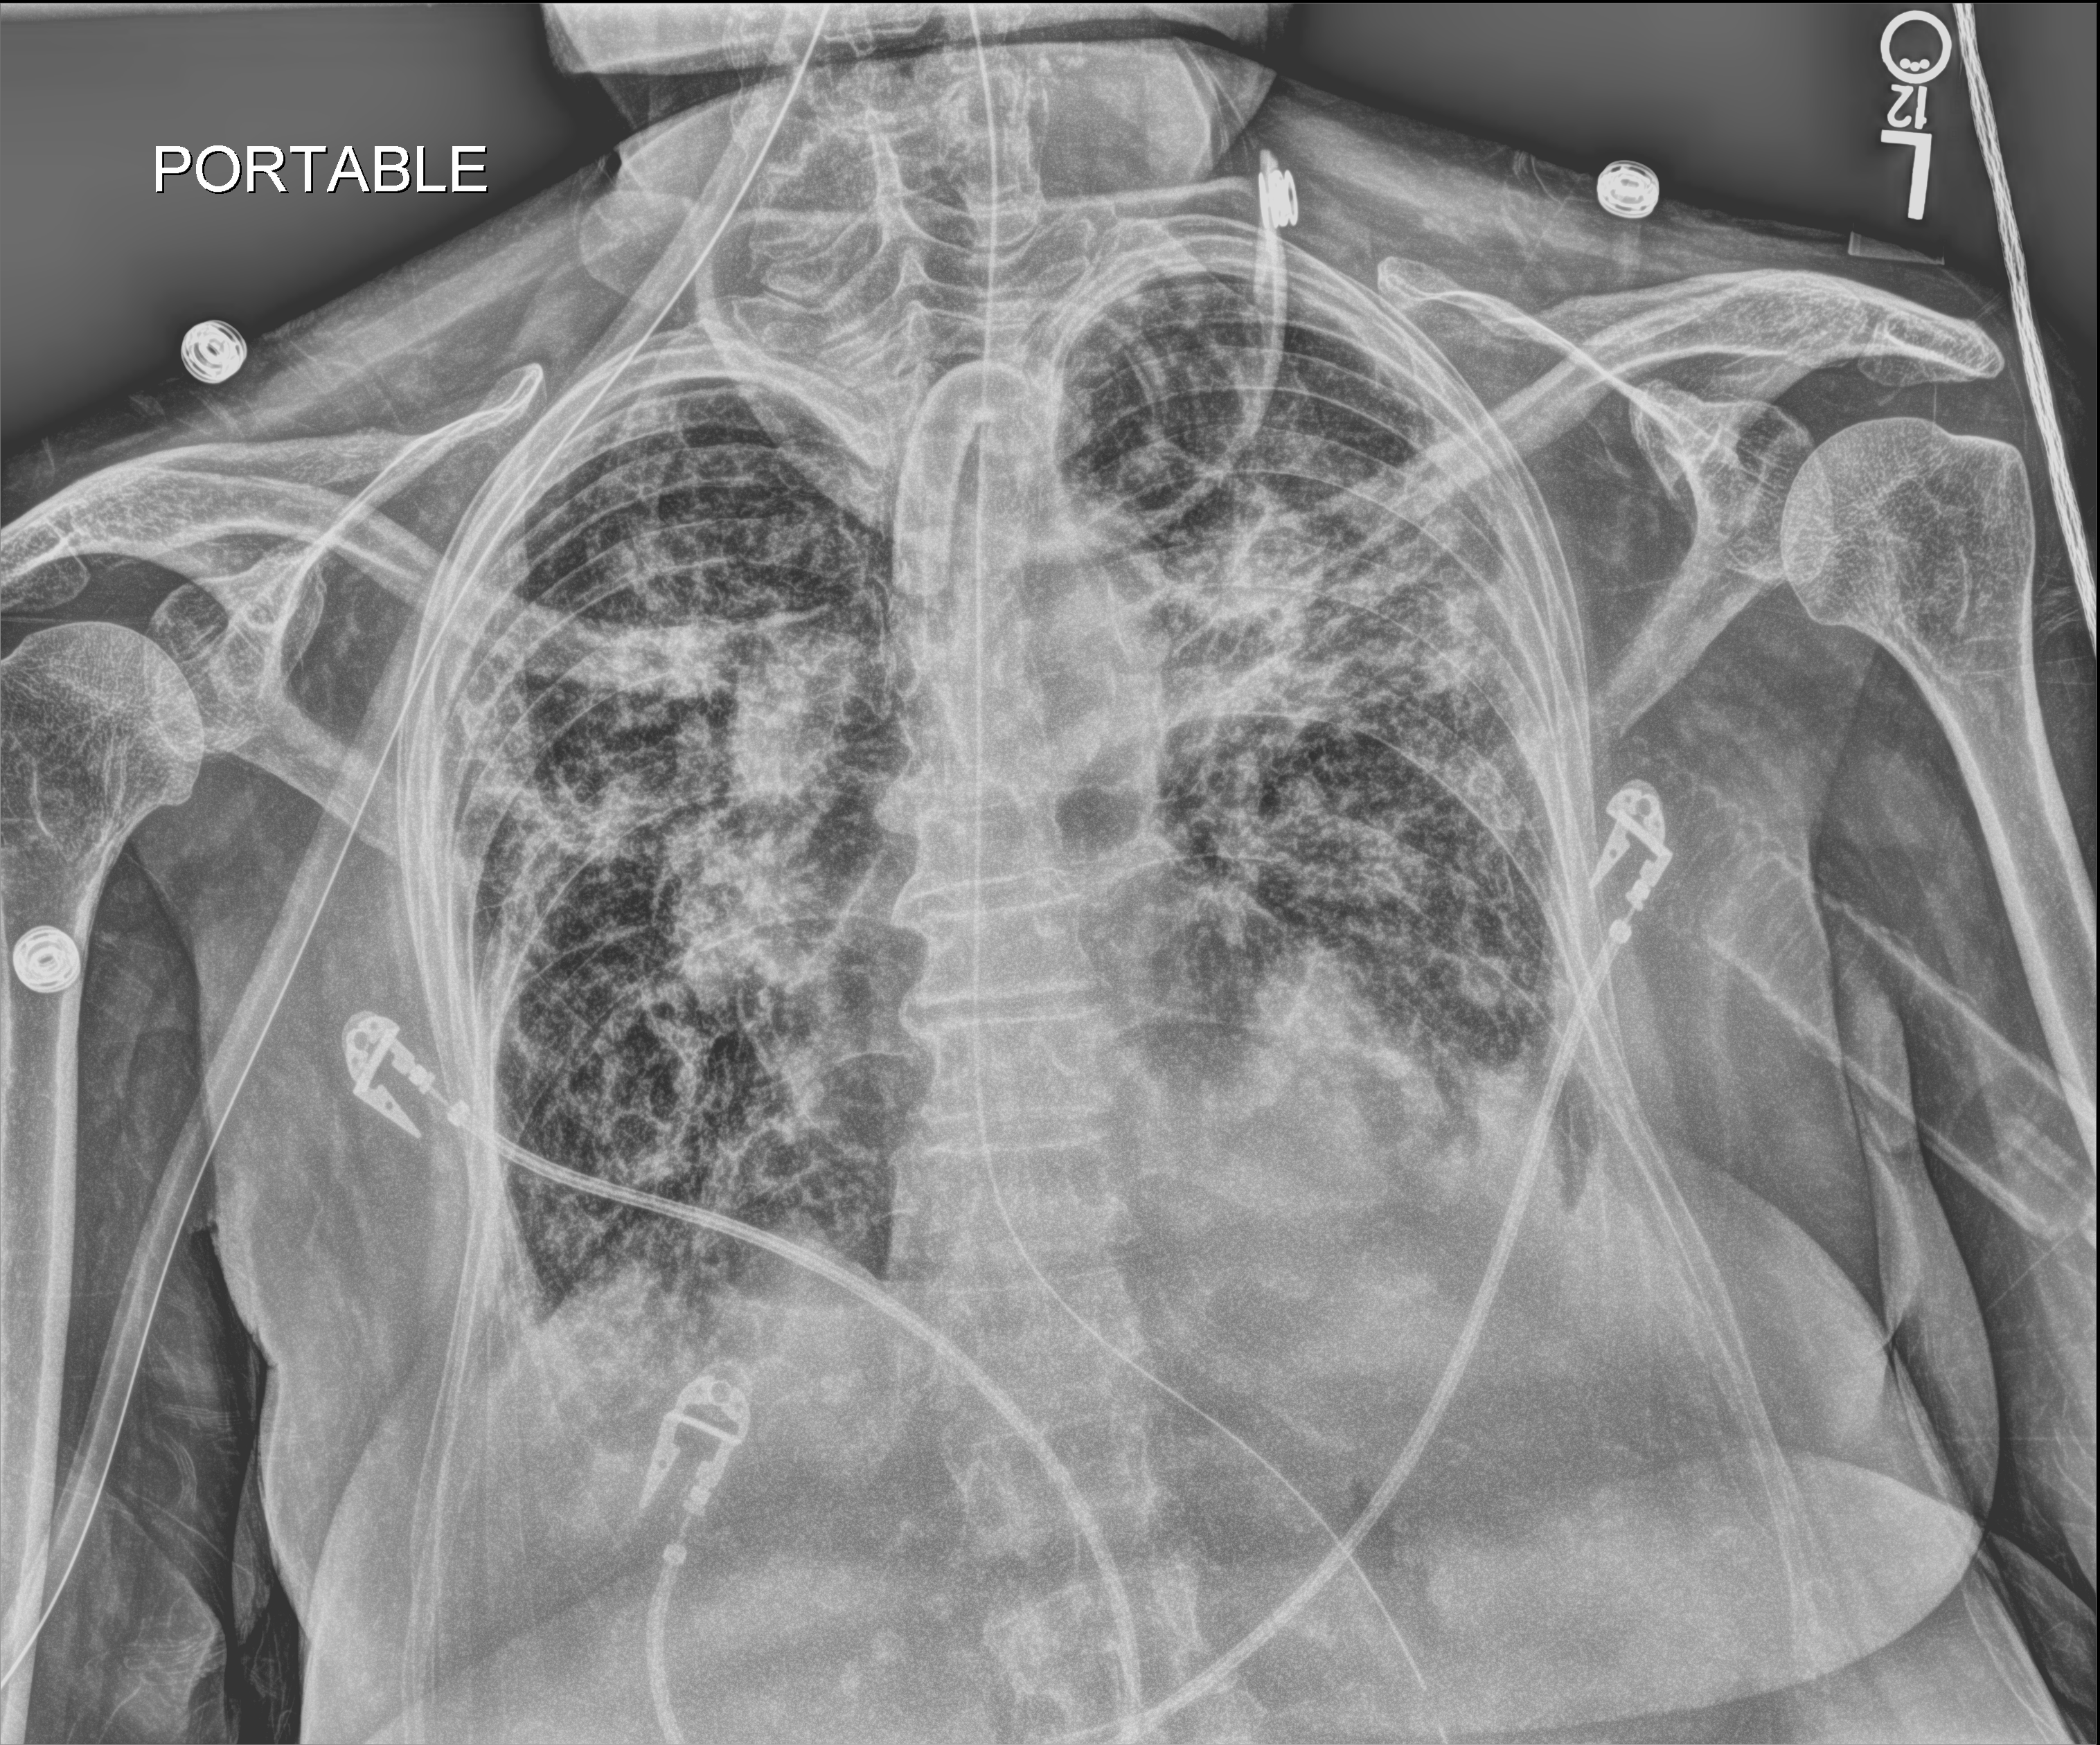
Chest X-ray (portable); anteroposterior (AP) projection. Patient hospitalised with COVID-19; female, aged 75–90 years.
Hospital-stay facts (about this admission, not read from this image; timing relative to this image not recorded):
- mechanically ventilated during this hospital stay: yes
- length of hospital stay: 70 days